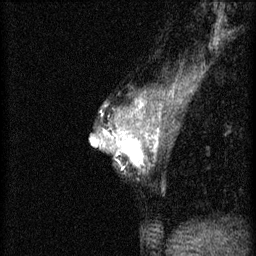
Breast MRI (dynamic contrast-enhanced), one sagittal slice. Slice 33 of 46 in the series (ordered by position). 3 images stored at this slice position (order not interpretable as contrast timing). 1.5 T. TE 4.2 ms, TR 8.2 ms. 2 mm slice thickness. 256 × 256 image matrix. Patient: female, 44 years.
Outlined on this slice (semi-automatically segmented with operator editing):
- analysis volume of interest (the breast-tissue region the enhancement analysis was run in; not a lesion): bounding box [x1, y1, x2, y2] px = [110, 128, 156, 175]
- tumour enhancement mask (voxels above the 70 % enhancement threshold inside the analysis volume of interest): [110, 130, 156, 173]